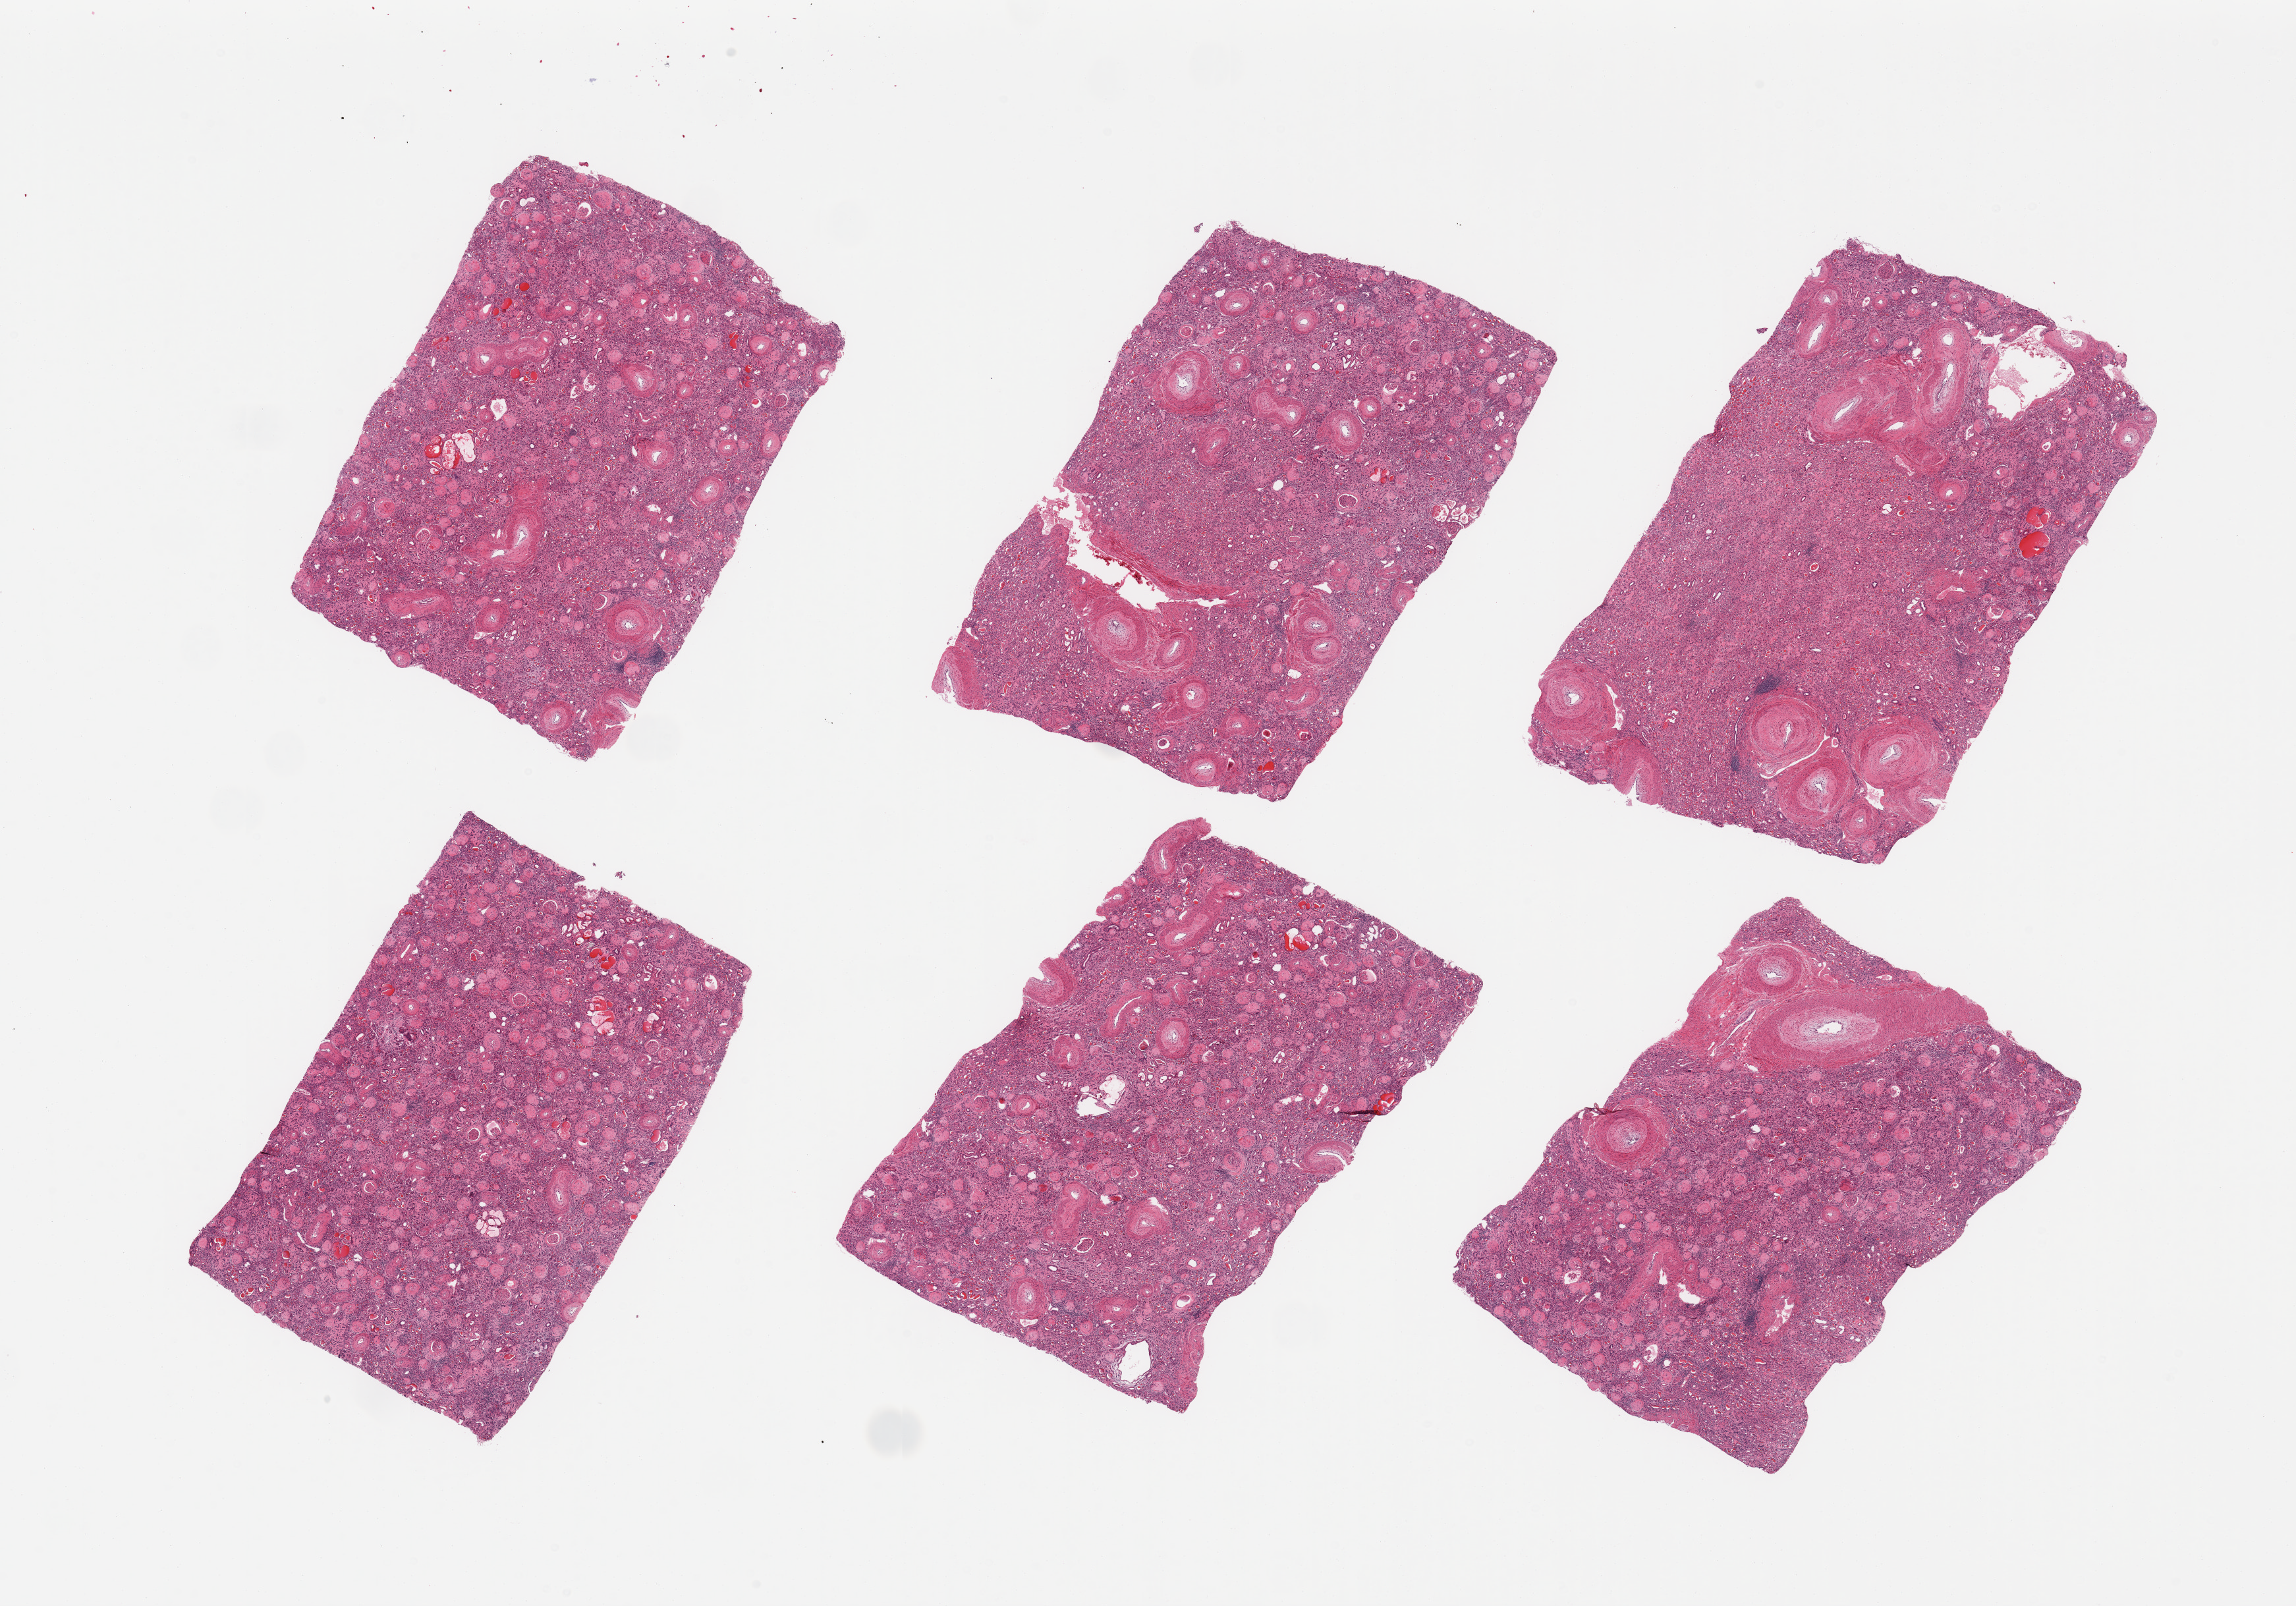
Digitized H&E-stained section, shown as a low-resolution overview of the whole scanned area (about 27.6 x 19.3 mm), PAXgene-fixed, paraffin-embedded tissue, target tissue: renal cortex, tissue donor sample. Male donor.
Review note (as recorded): 6 pieces; severe arterial, arteriolar and glomerular sclerosis with hyalin casts; 'end-stage' kidney.